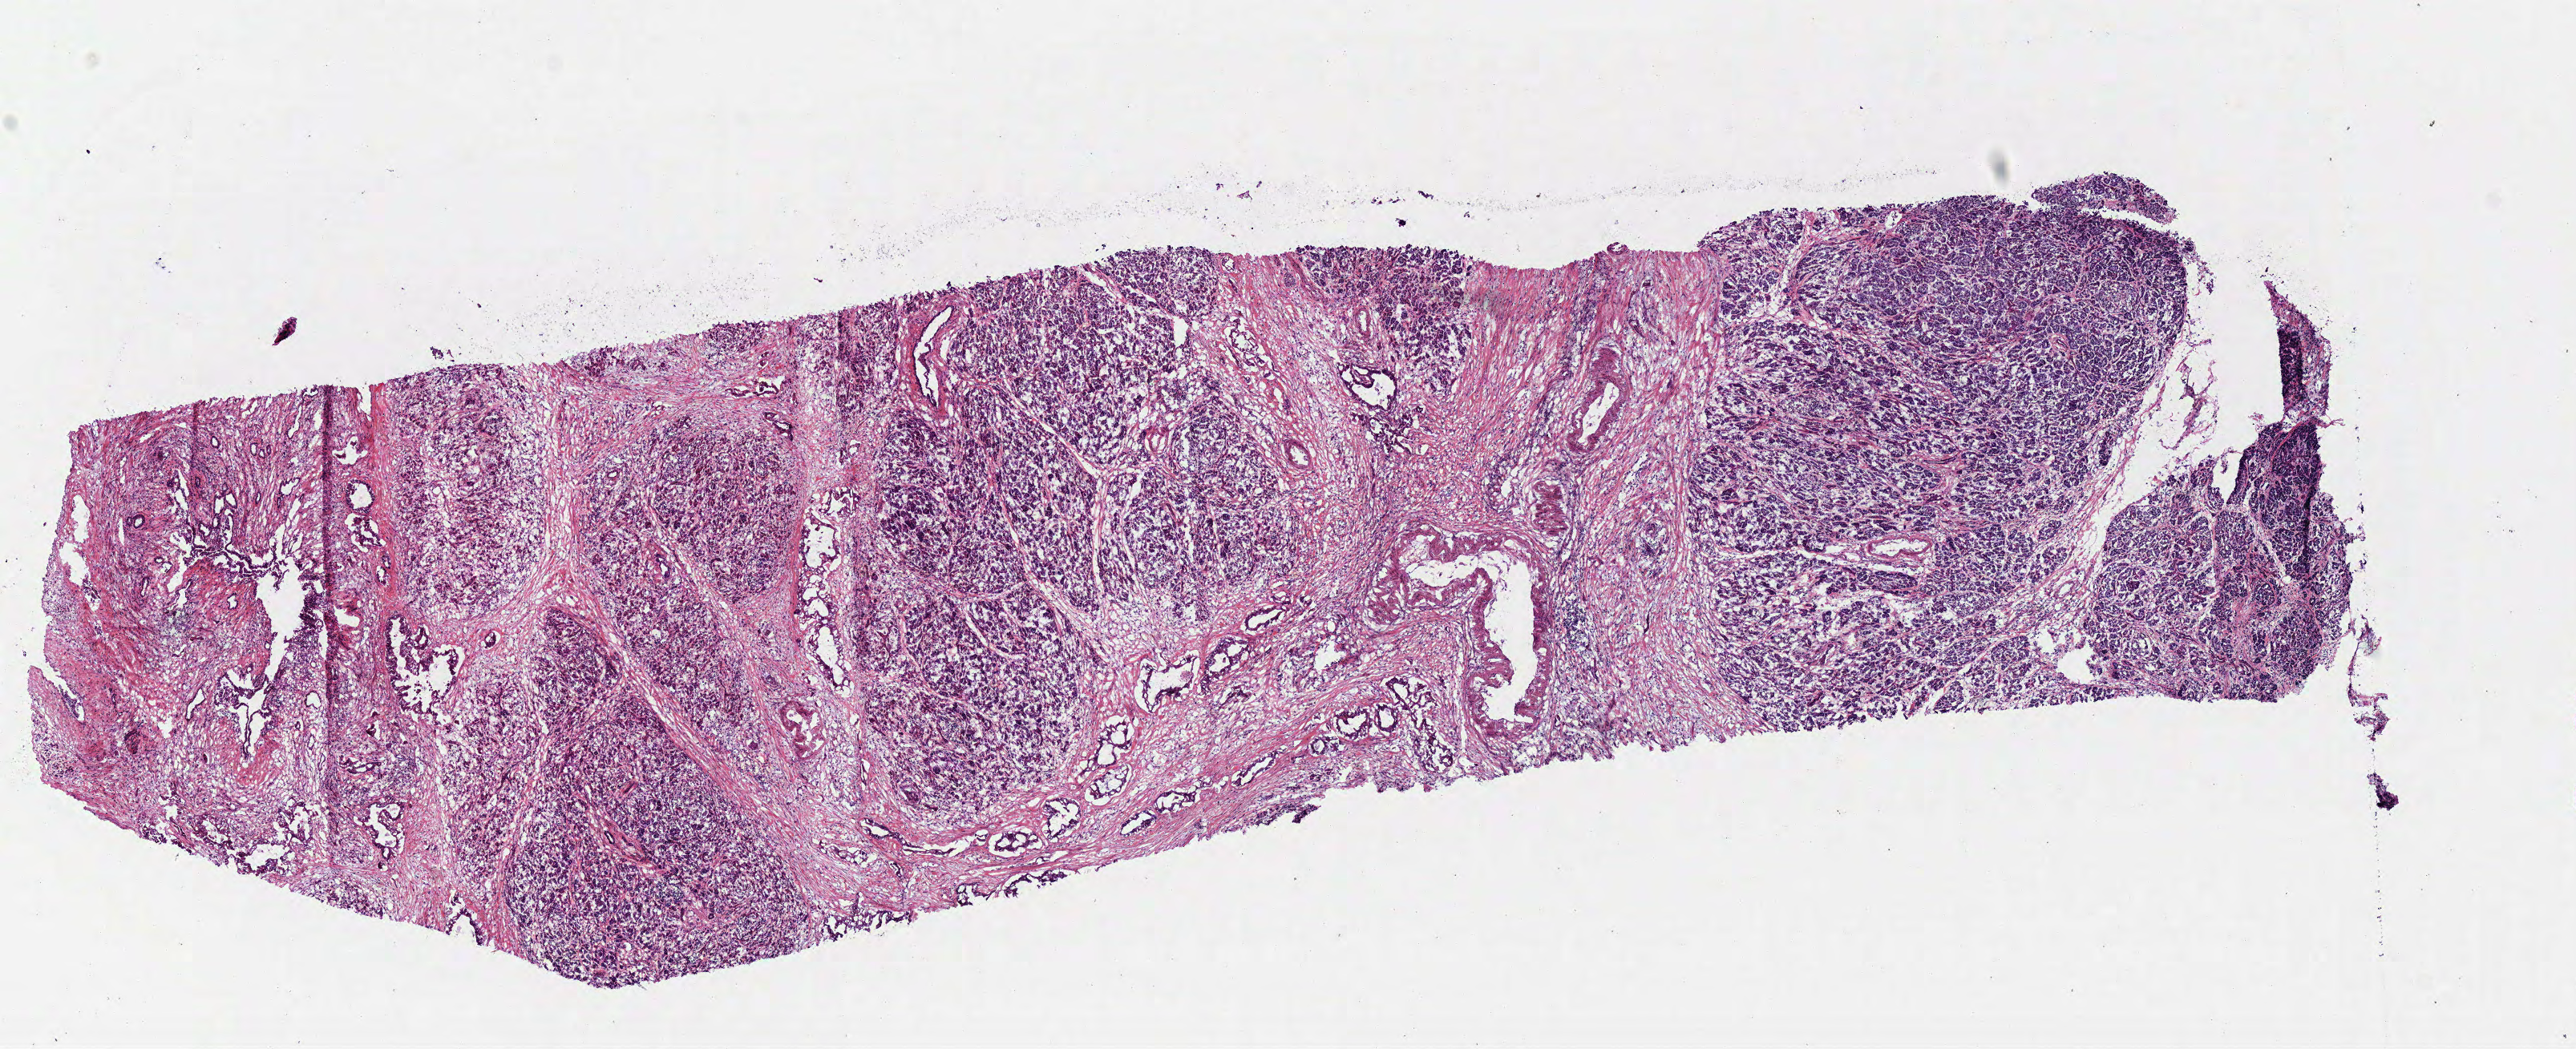
H&E whole-slide image, low-resolution overview of the scanned area, about 12.7 x 5.2 mm (from a 40x scan), frozen section from the bottom of the tissue portion, sample: primary tumour, pancreas. Female, age 73 years at initial diagnosis. Histologic grade: G2 (moderately differentiated). Slide review estimates, as recorded: tumour cells 10%, tumour nuclei 10%, normal cells 70%, stromal cells 20%, necrosis 0%.
Pathologic diagnosis: Infiltrating duct carcinoma, NOS (head of pancreas). AJCC pathologic stage: III (5th edition).